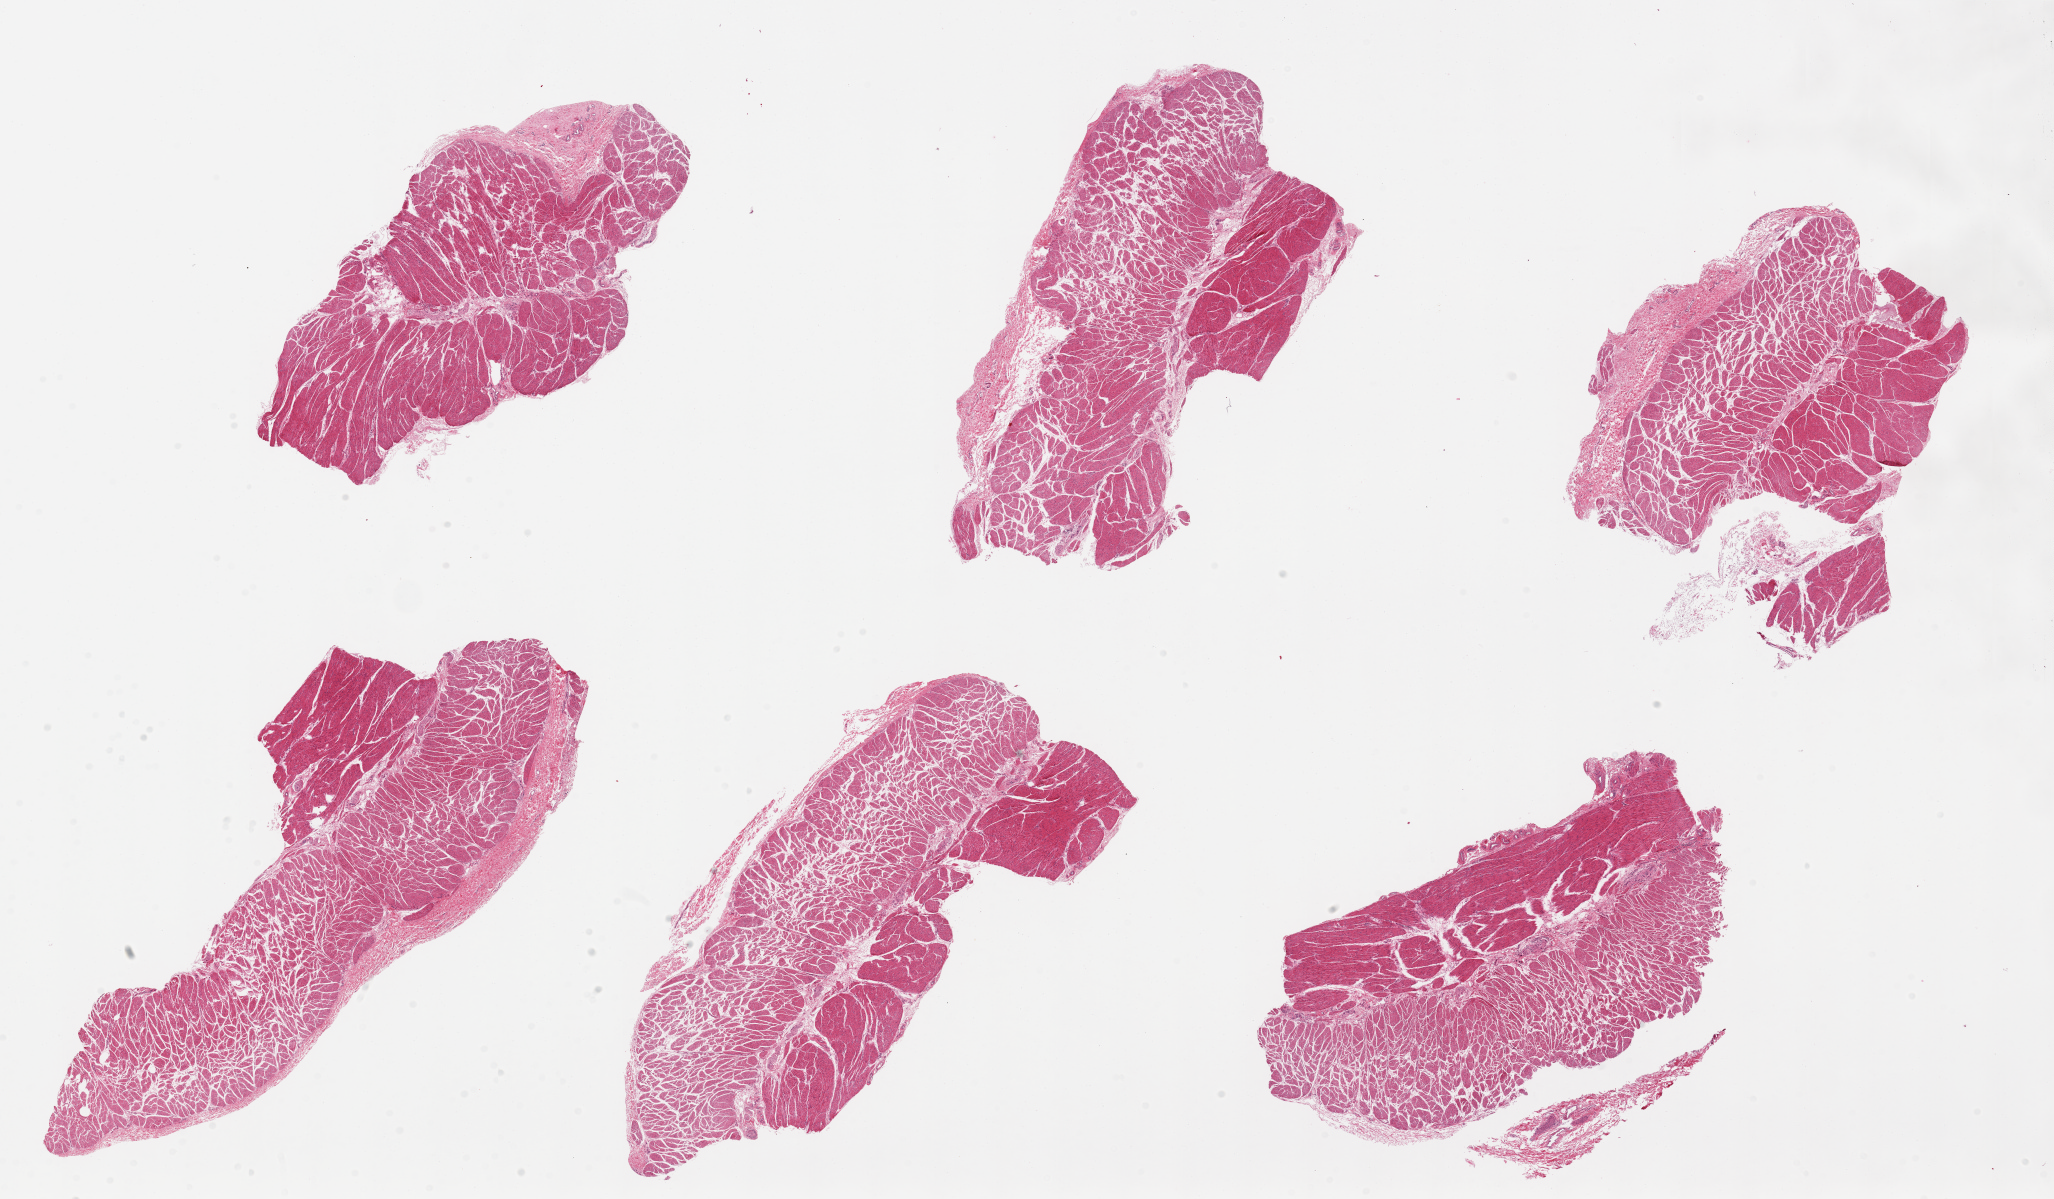
Hematoxylin and eosin (H&E) whole-slide image — a low-resolution overview of the entire scanned area, about 32.5 x 19.0 mm (slide scanned at 20x); PAXgene-fixed, paraffin-embedded tissue; section of esophageal muscle (target tissue); tissue donor sample. Donor: male.
- pathologist's review note for this sample: 6 pieces, up to 11x5mm; Well trimmed